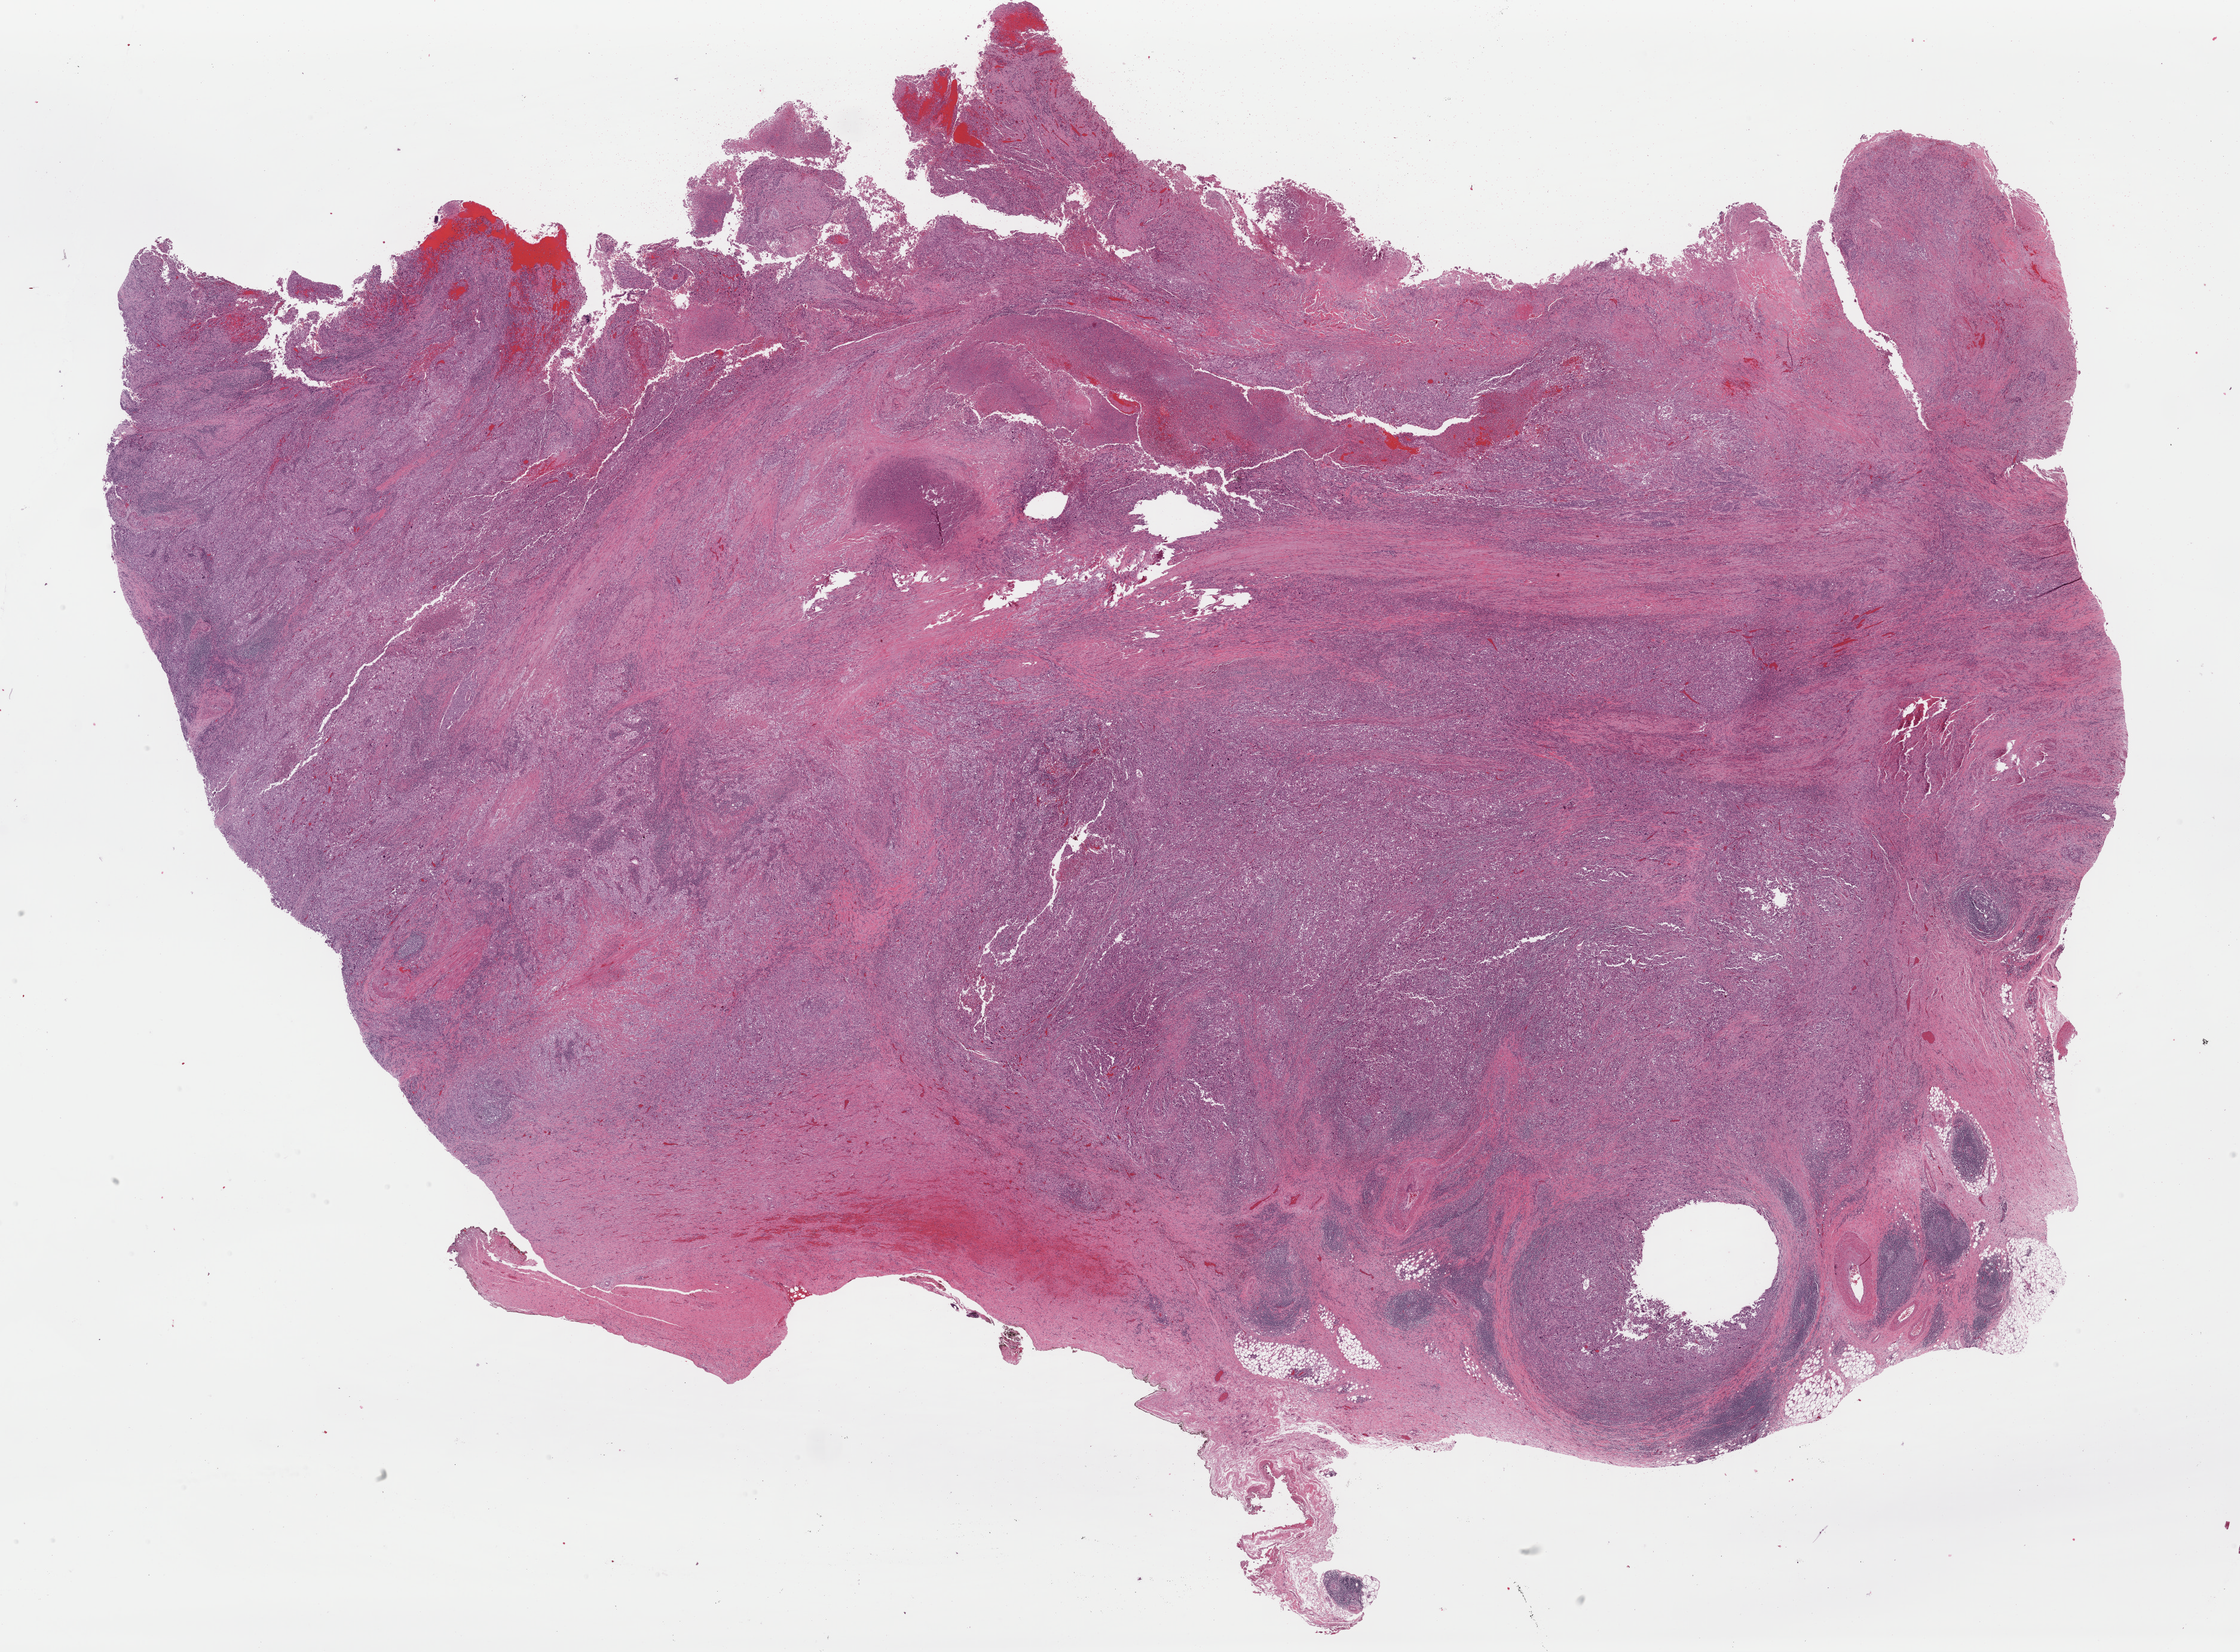
H&E whole-slide image — shown as a low-resolution overview of the whole scanned area (about 29.6 x 21.8 mm, slide scanned at 40x), FFPE section, primary tumour sample from the bladder. Patient: male, age at initial diagnosis 66 years. Histologic grade: high grade.
TNM: T3a N0 MX. Lymph nodes positive (case pathology): 0 of 16 examined. Pathologic diagnosis: Transitional cell carcinoma (lateral wall of bladder). AJCC pathologic stage: III (7th edition).